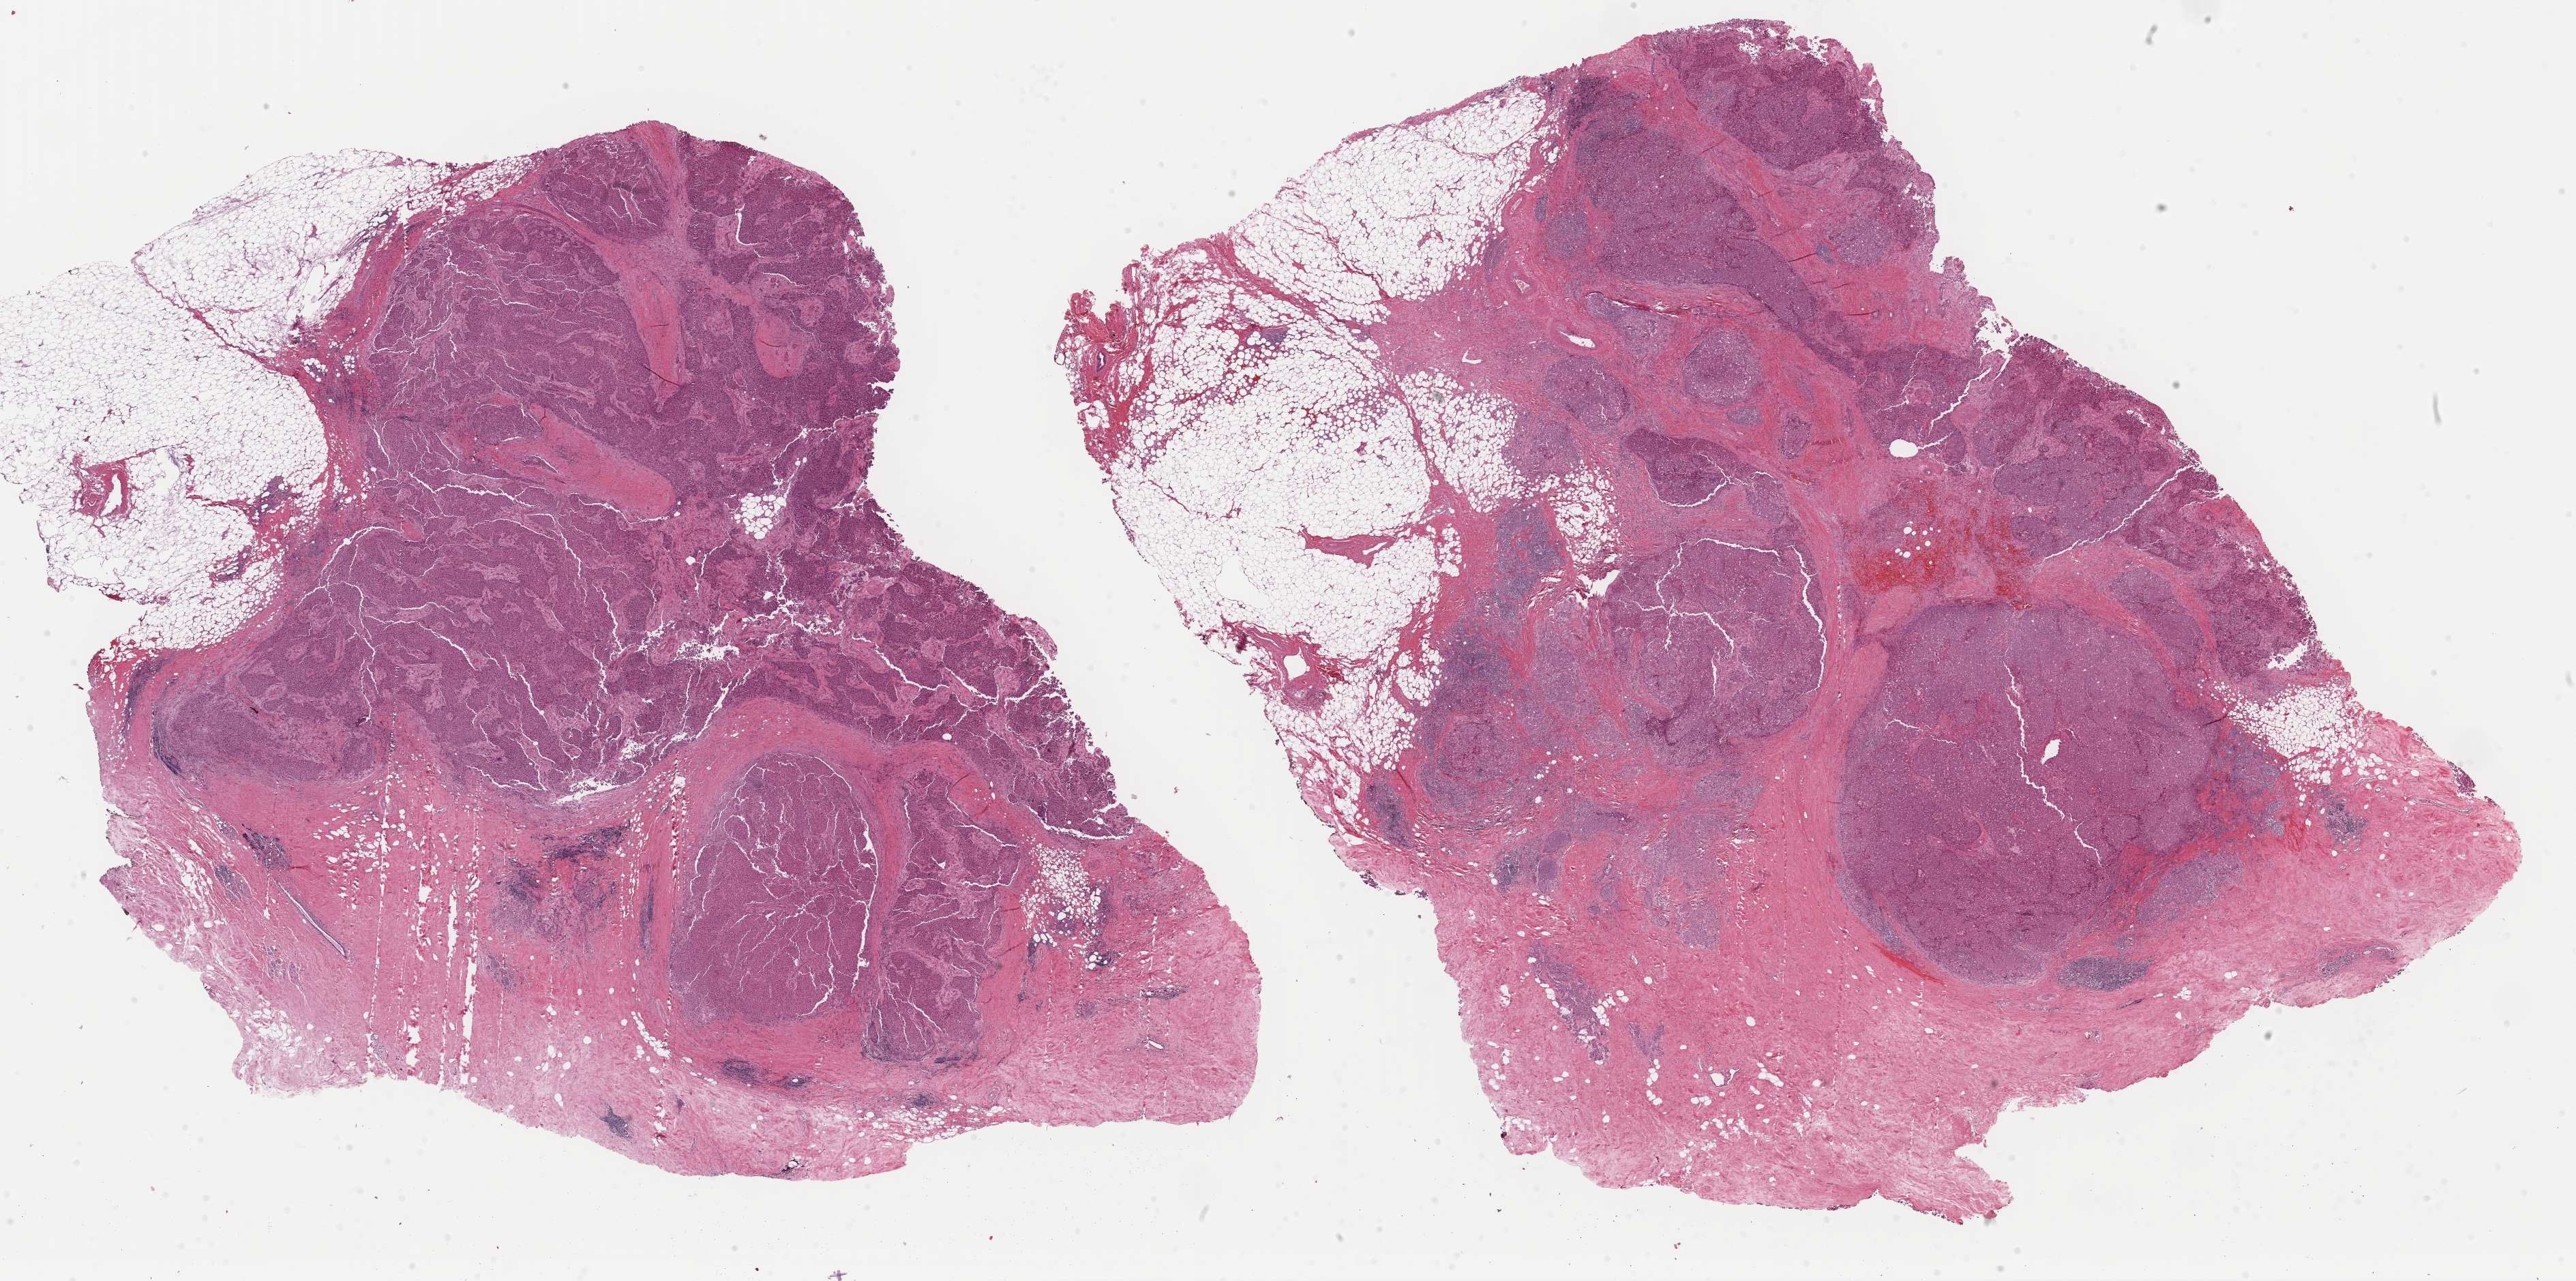
H&E whole-slide image — shown as a low-resolution overview of the whole scanned area (about 29.8 x 14.8 mm); formalin-fixed paraffin-embedded (FFPE) diagnostic section; breast, primary tumour sample. Patient: female, age at initial diagnosis 62 years.
Laterality: left. Pathologic diagnosis: Lobular carcinoma, NOS. Lymph nodes positive (case pathology): 1 of 3 examined. AJCC pathologic stage: IIA (6th edition).